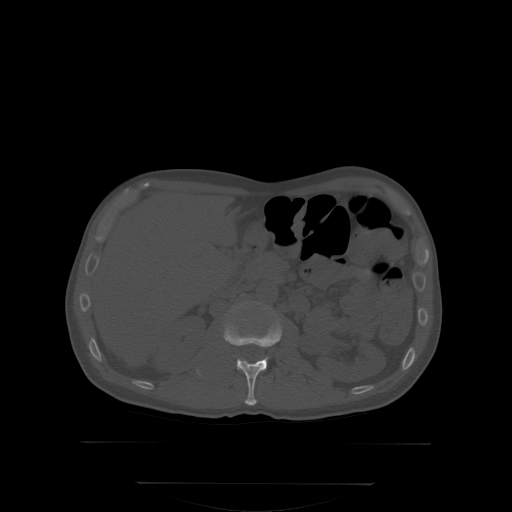
CT including the spine, one axial slice; position 149 of 350 along the scan axis; bone window (W 1800 / L 400 HU); 512 × 512 image matrix, field of view 500 × 500 mm. Male patient, age 58 years. From the clinical record (not read from this slice): primary cancer: prostate; vertebrae with lytic lesions (as recorded): L1.
Annotated regions visible in this slice (semi-automatically segmented with operator editing):
- L1 vertebra: bounding box <224,321,280,405> (left, top, right, bottom; pixels)